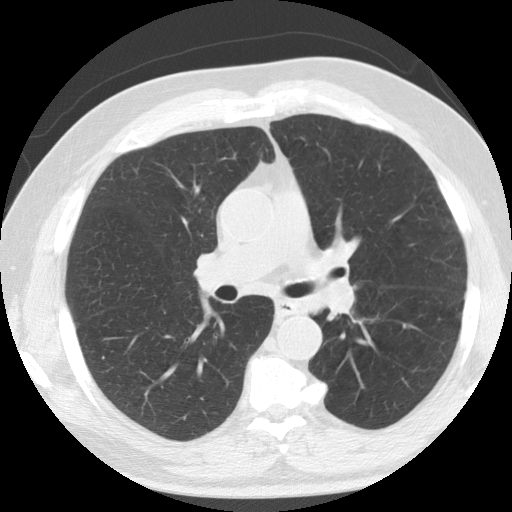
Low-dose screening chest CT, one axial slice; position 79 of 133 along the scan axis; lung window (W 1500 / L -600 HU); 2.5 mm slice thickness; 512 × 512 image matrix.
Annotated regions visible in this slice (outlined manually by an expert reader):
- lesion 1 (tumor, upper lobe of left lung): bounding box <323,280,355,311> (left, top, right, bottom; pixels)